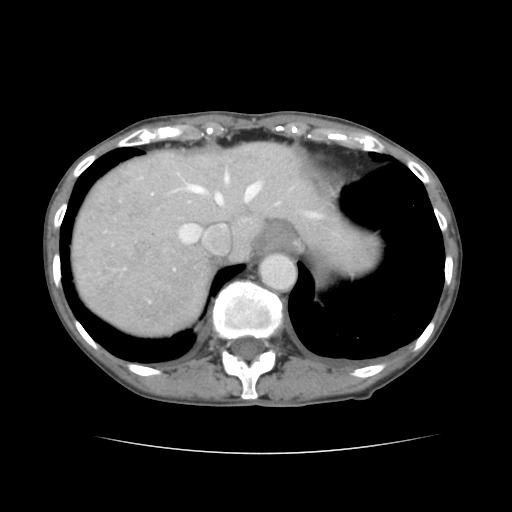
Contrast-enhanced abdominal CT, one axial slice; position 118 of 136 along the scan axis; 120 kVp; intravenous contrast given; soft-tissue window (W 400 / L 40 HU); 512 × 512 image matrix, field of view 319 × 319 mm. Female patient, age 77 years. Case-level facts recorded for this patient, not image findings: diagnosis: colorectal cancer liver metastases, imaged before liver resection; multiple liver metastases: yes; largest metastasis: 3 cm; disease in both lobes: no.
Structures marked on this image (expert manual segmentation):
- hepatic veins: bounding box [x1, y1, x2, y2] px = [137, 175, 316, 246]
- liver: [73, 143, 365, 334]
- planned liver remnant (the part of the liver to remain after resection): [174, 143, 368, 257]